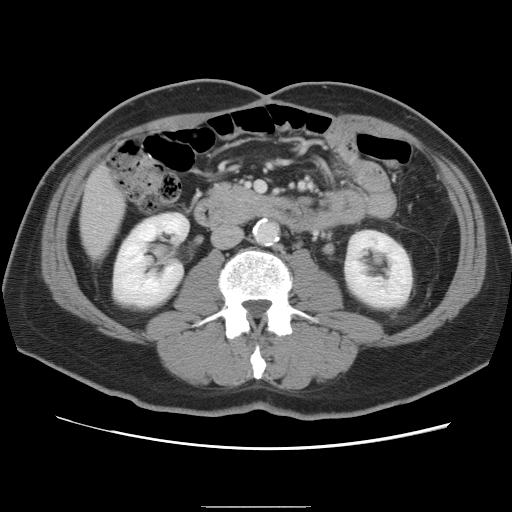
Contrast-enhanced abdominal CT, one axial slice; position 21 of 87 along the scan axis; 120 kVp; intravenous contrast given; soft-tissue window (W 400 / L 40 HU); 5 mm slice thickness; 512 × 512 image matrix. Male patient, age 63 years. From the clinical record (not read from this slice): diagnosis: colorectal cancer liver metastases, imaged before liver resection; multiple liver metastases: no; largest metastasis: 9 cm.
Annotated regions visible in this slice (outlined manually by an expert reader):
- liver: bounding box <81,168,125,259> (left, top, right, bottom; pixels)
- planned liver remnant (the part of the liver to remain after resection): <82,168,126,259>